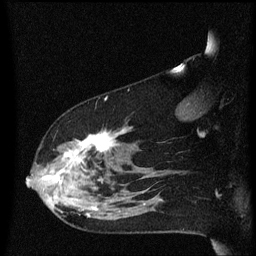
Breast MRI (dynamic contrast-enhanced), one sagittal slice; slice 44 of 60 in the series (ordered by position); dynamic contrast-enhanced series, image 2 of 3 at this slice position (ordered by acquisition); 1.5 T; TE 4.2 ms, TR 8.4 ms; 256 × 256 image matrix. Female patient, age 48 years.
Outlined on this slice (semi-automatic segmentation, software-assisted and operator-edited):
- analysis volume of interest (the breast-tissue region the enhancement analysis was run in; not a lesion): bounding box [x1, y1, x2, y2] px = [31, 128, 134, 225]
- tumour enhancement mask (voxels above the 70 % enhancement threshold inside the analysis volume of interest): [55, 132, 124, 217]